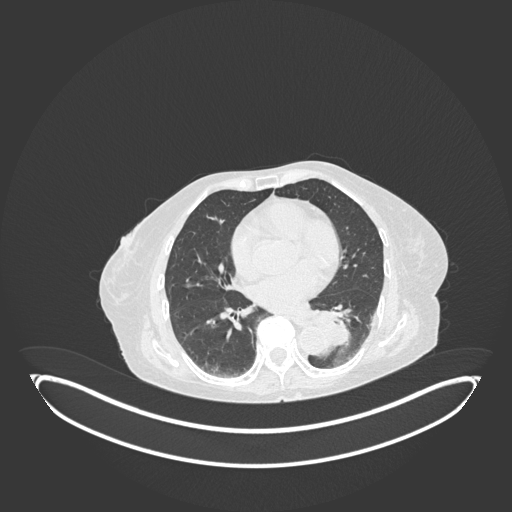
Chest CT, one axial slice; position 49 of 189 along the scan axis; 120 kVp; lung window (W 1500 / L -600 HU); 1 mm slice thickness; 512 × 512 image matrix, field of view 500 × 500 mm. Female patient, age 82 years. From the clinical record (not read from this slice): clinical TNM (as recorded): T1b N0 M1.
Annotated regions visible in this slice (rectangle marked by the reading radiologist):
- lung tumour (recorded histology: adenocarcinoma): bounding box [x1, y1, x2, y2] px = [310, 310, 355, 357]